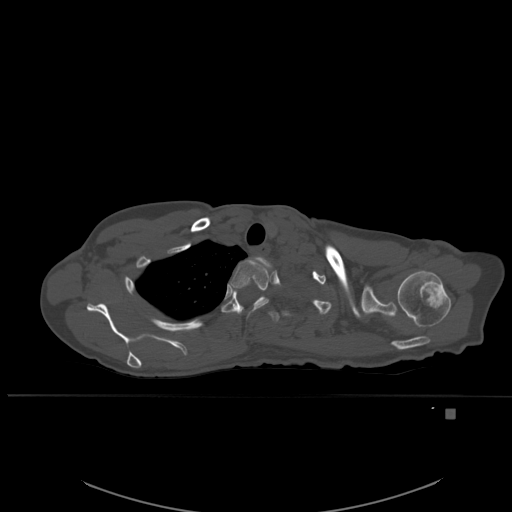
CT including the spine, one axial slice; slice 431 of 537 in the series (ordered by position); bone window (W 1800 / L 400 HU); 1.5 mm slice thickness; 512 × 512 image matrix, field of view 440 × 440 mm. Female patient, age 45 years. From the clinical record (not read from this slice): primary cancer: lung.
Annotated regions visible in this slice (semi-automatically segmented with operator editing):
- T1 vertebra: box from (x=260, y=258) to (x=269, y=265) px
- T2 vertebra: (x=230, y=259)–(x=270, y=320)
- T3 vertebra: (x=222, y=289)–(x=280, y=323)